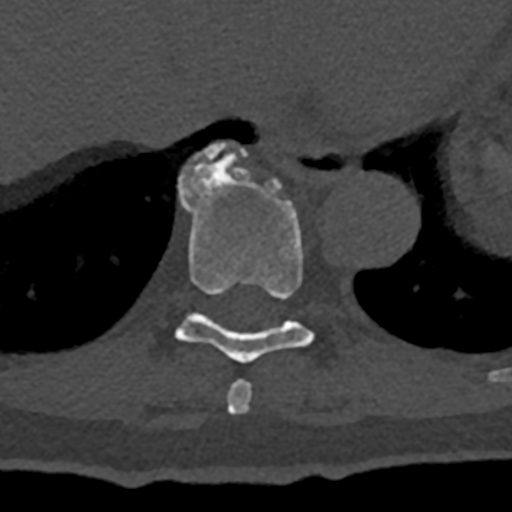
CT including the spine, one axial slice. Position 652 of 797 along the scan axis. 120 kVp. Bone window (W 1800 / L 400 HU). 512 × 512 image matrix, field of view 160 × 160 mm. Patient: male, 74 years. From the clinical record (not read from this slice): primary cancer: renal.
Annotated regions visible in this slice (semi-automatically segmented with operator editing):
- T10 vertebra: bounding box <178,142,247,196> (left, top, right, bottom; pixels)
- T8 vertebra: <227,380,252,415>
- T9 vertebra: <175,157,314,363>